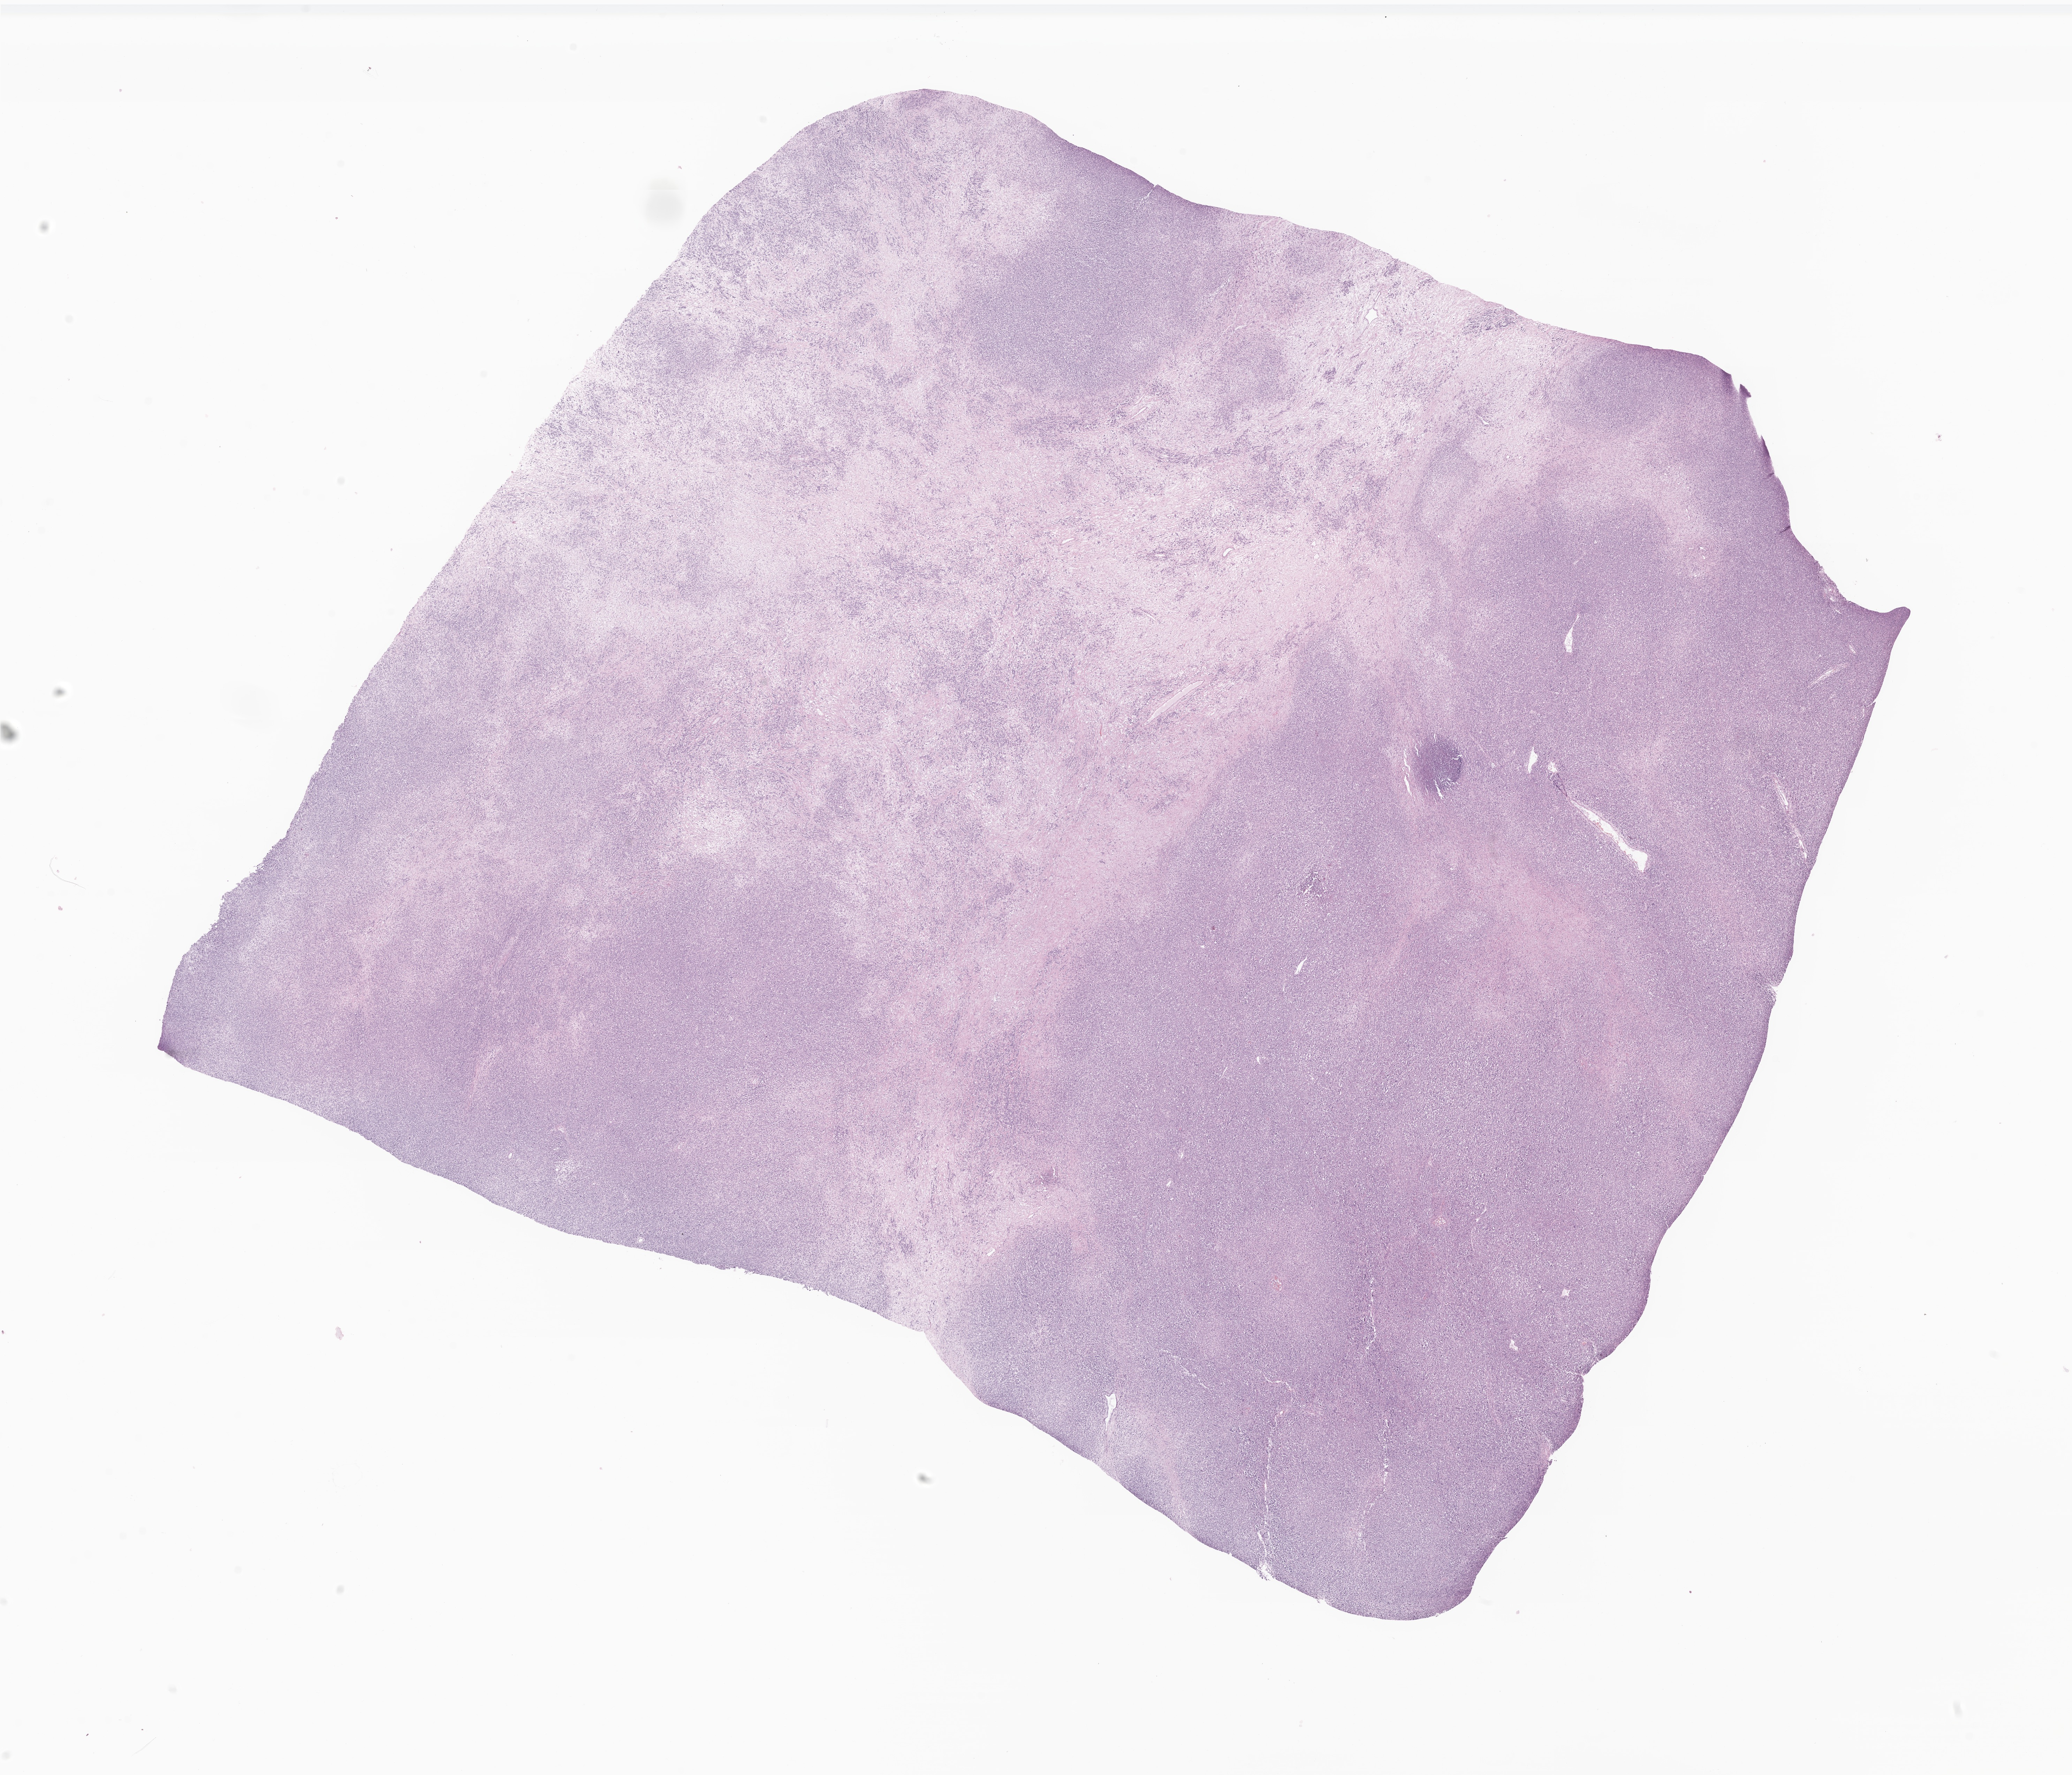
Whole-slide image, H&E stain of tumor tissue from the colon, low-resolution overview of the scanned area, about 25.1 x 21.5 mm, formalin-fixed paraffin-embedded section. Patient female; age 212 months (17 years 8 months).
• diagnosis: Carcinoma, NOS